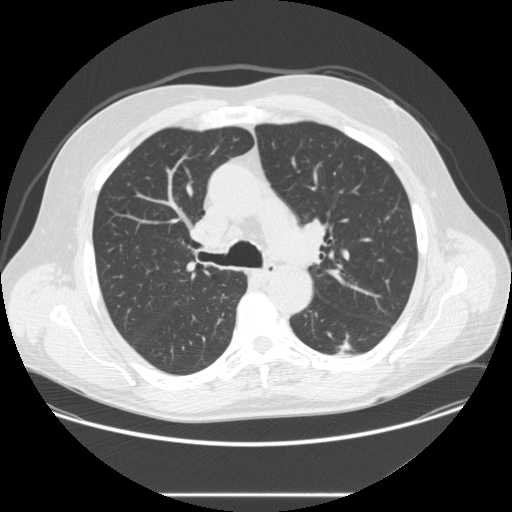
Low-dose screening chest CT, one axial slice. Slice 171 of 262 in the series (ordered by position). Reconstruction kernel STANDARD. Lung window (W 1500 / L -600 HU). 512 × 512 image matrix, field of view 420 × 420 mm.
Structures marked on this image (outlined manually by an expert reader):
- lesion 1 (tumor, lower lobe of left lung): box from (x=337, y=341) to (x=352, y=355) px